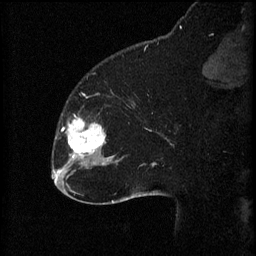
Breast MRI (dynamic contrast-enhanced), one sagittal slice; slice 18 of 60 in the series (ordered by position); 3 images stored at this slice position (order not interpretable as contrast timing); 1.5 T; TE 4.2 ms, TR 8.2 ms; 256 × 256 image matrix, field of view 180 × 180 mm. Female patient, age 32 years.
Outlined on this slice (semi-automatically segmented with operator editing):
- analysis volume of interest (the breast-tissue region the enhancement analysis was run in; not a lesion): bounding box <58,112,111,165> (left, top, right, bottom; pixels)
- tumour enhancement mask (voxels above the 70 % enhancement threshold inside the analysis volume of interest): <68,116,106,159>